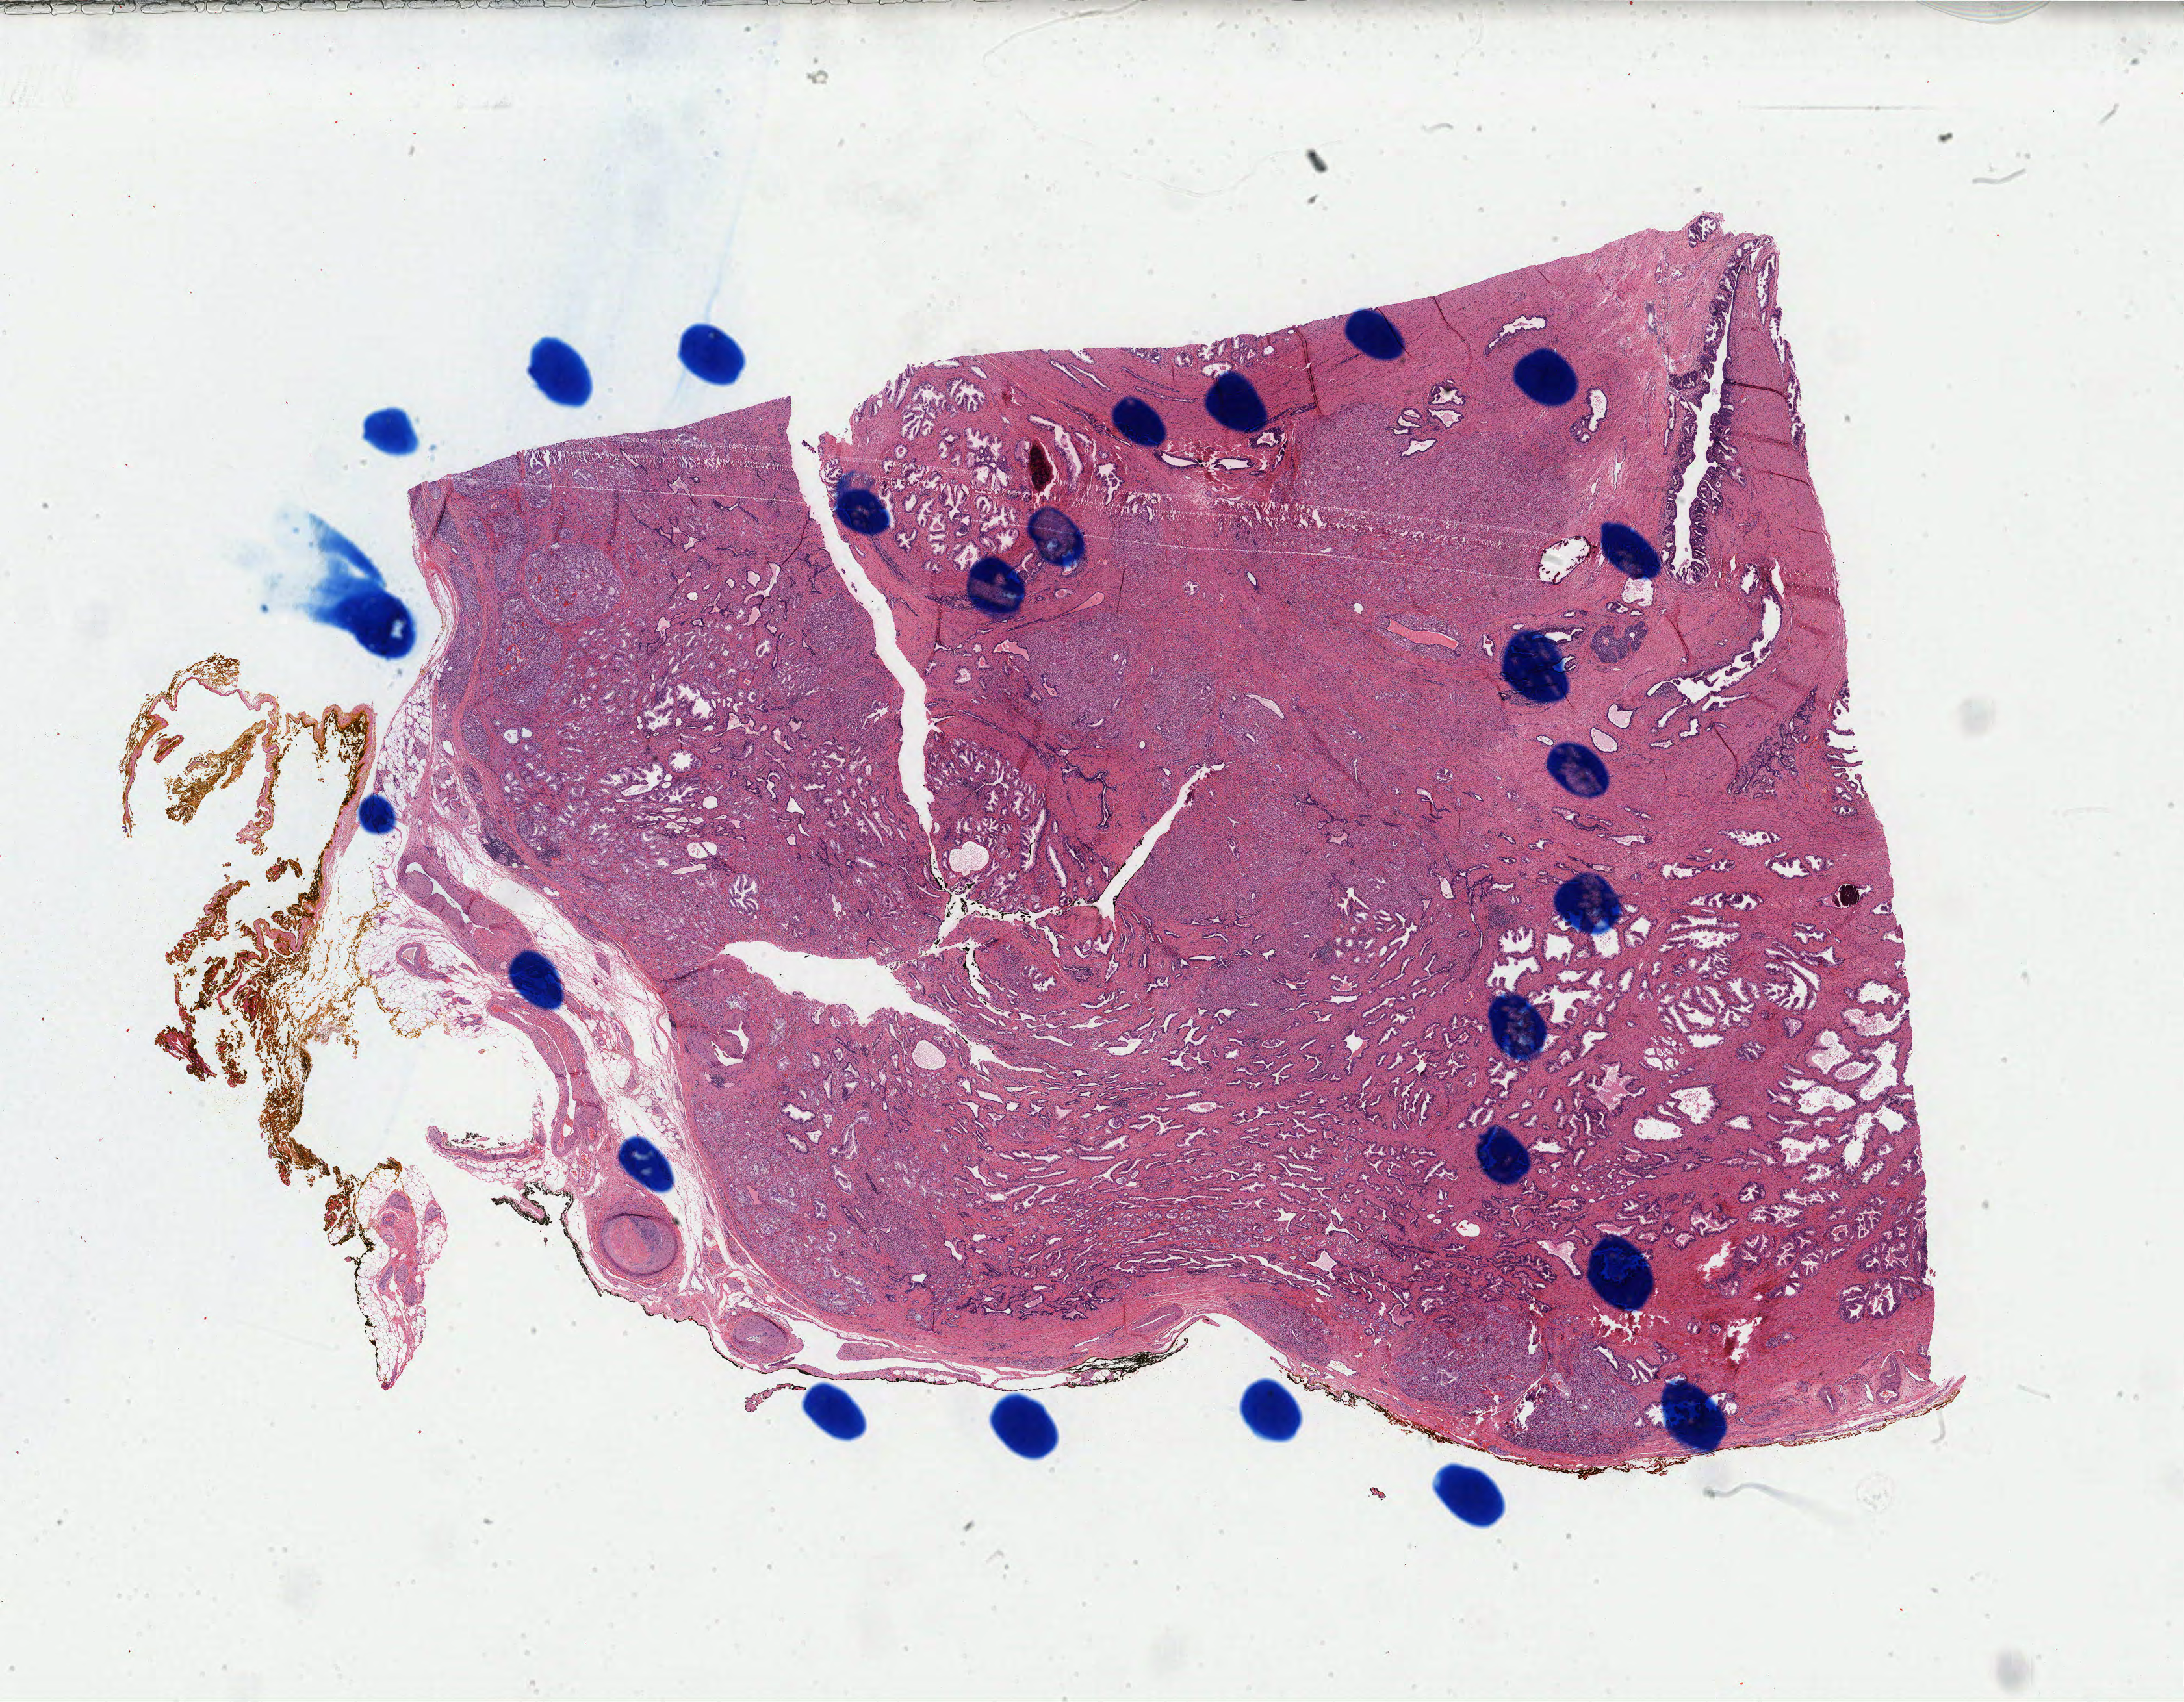
Whole-slide histology image, H&E, a low-resolution overview of the entire scanned area, about 26.7 x 20.8 mm, FFPE section, primary tumour sample from the prostate. Male, age 55 years at initial diagnosis. Gleason score: 9 (4+5).
Diagnosis: Adenocarcinoma, NOS (prostate gland). Lymph nodes positive (case pathology): 0 of 9 examined.